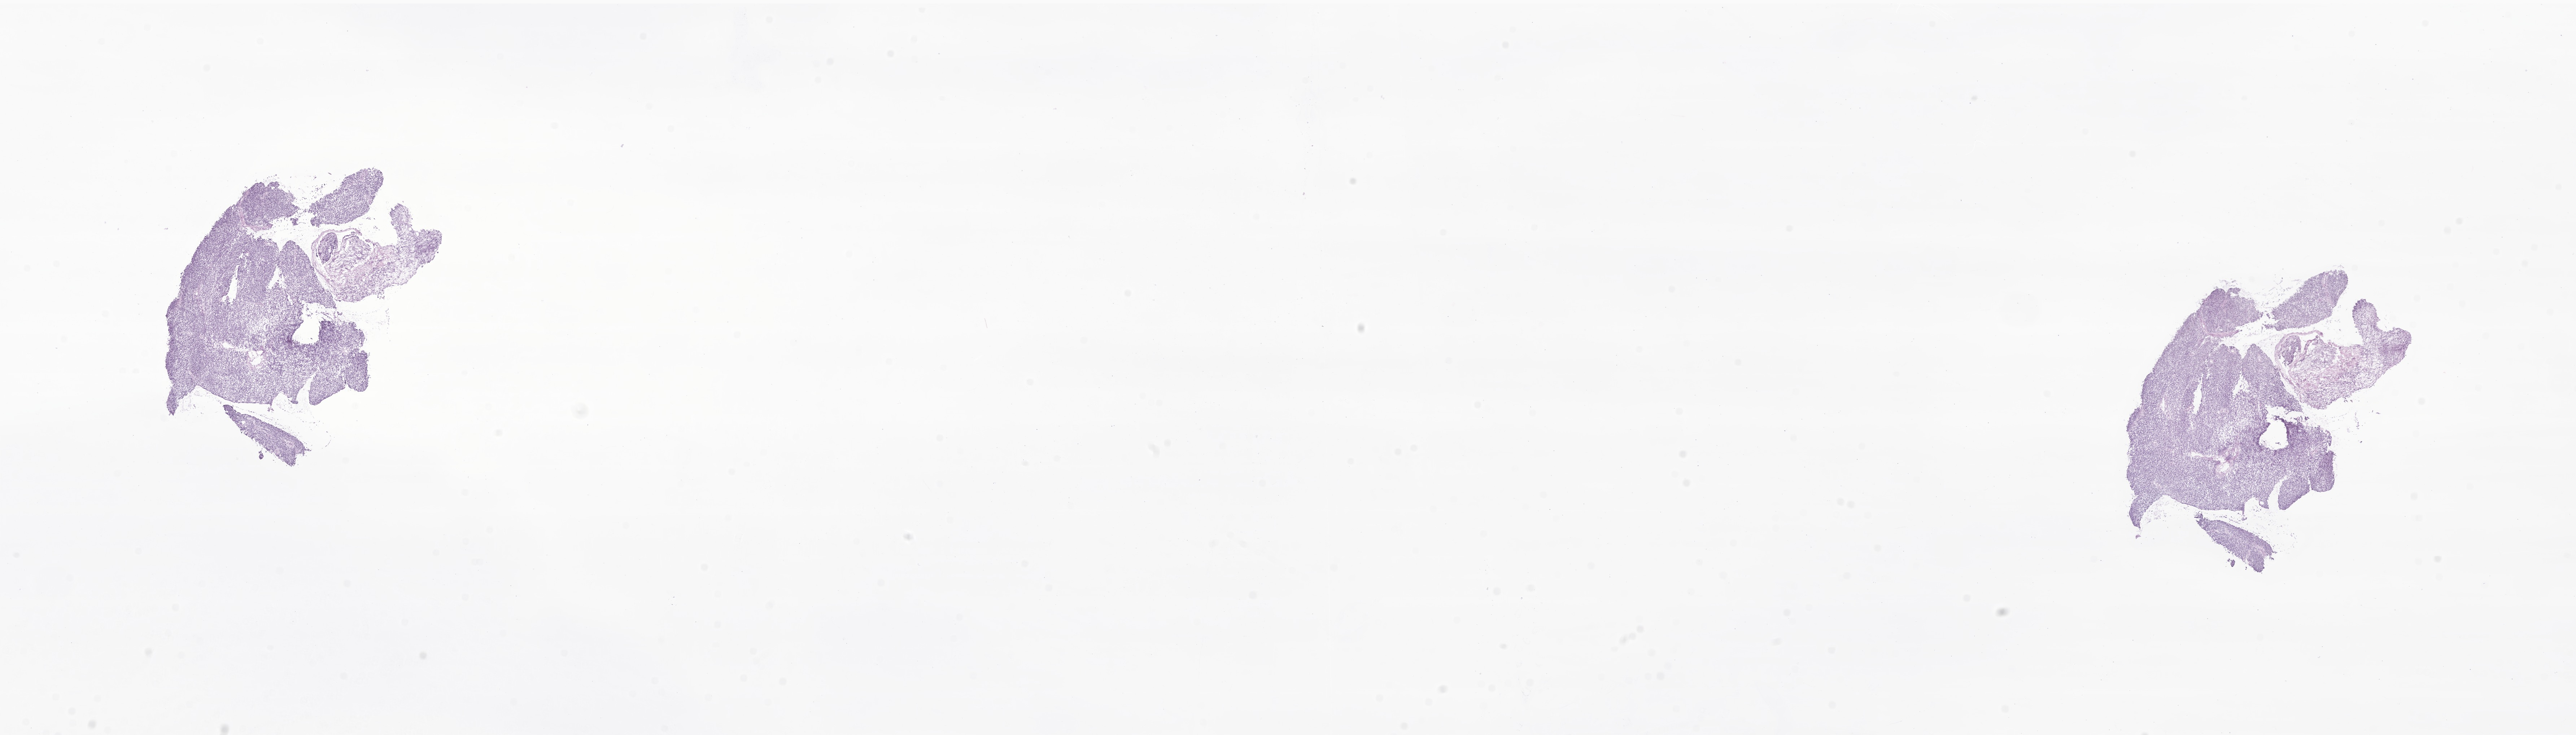
Digitized hematoxylin and eosin (H&E)-stained section of tumor tissue from the eye, a low-resolution overview of the entire scanned area, about 30.1 x 8.6 mm. Frozen section. Patient: female, age 90 months.
Diagnosis: Alveolar rhabdomyosarcoma.